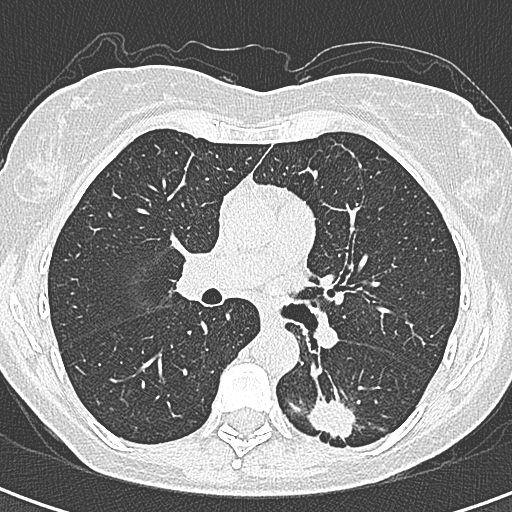
Axial slice from a low-dose chest CT screening exam. Baseline screening round. Lung window (W 1500 / L -600 HU). 1 mm slice thickness. Lung (sharp) reconstruction kernel (B80f). 120 kVp. Slice 134 of 328 in the series. 512 × 512 image matrix, field of view 284 × 284 mm. Female, age 58 years at enrolment. Former smoker at enrolment.
• Lesion marked by an expert reader, bounding box [x1, y1, x2, y2] px = [296, 387, 366, 456].
• The screening reader recorded 2 non-calcified nodules or masses ≥4 mm on this exam; which of them this box marks is not recorded.
• Official screen result: positive, change unspecified: nodule(s) >= 4 mm or enlarging nodule(s), mass(es), or other non-specific abnormalities suspicious for lung cancer.
• Later outcome: lung cancer diagnosed 22 days after this screen — adenocarcinoma, NOS, left lower lobe, moderately differentiated (G2), stage IA (AJCC 6th edition), 25 mm at pathology.